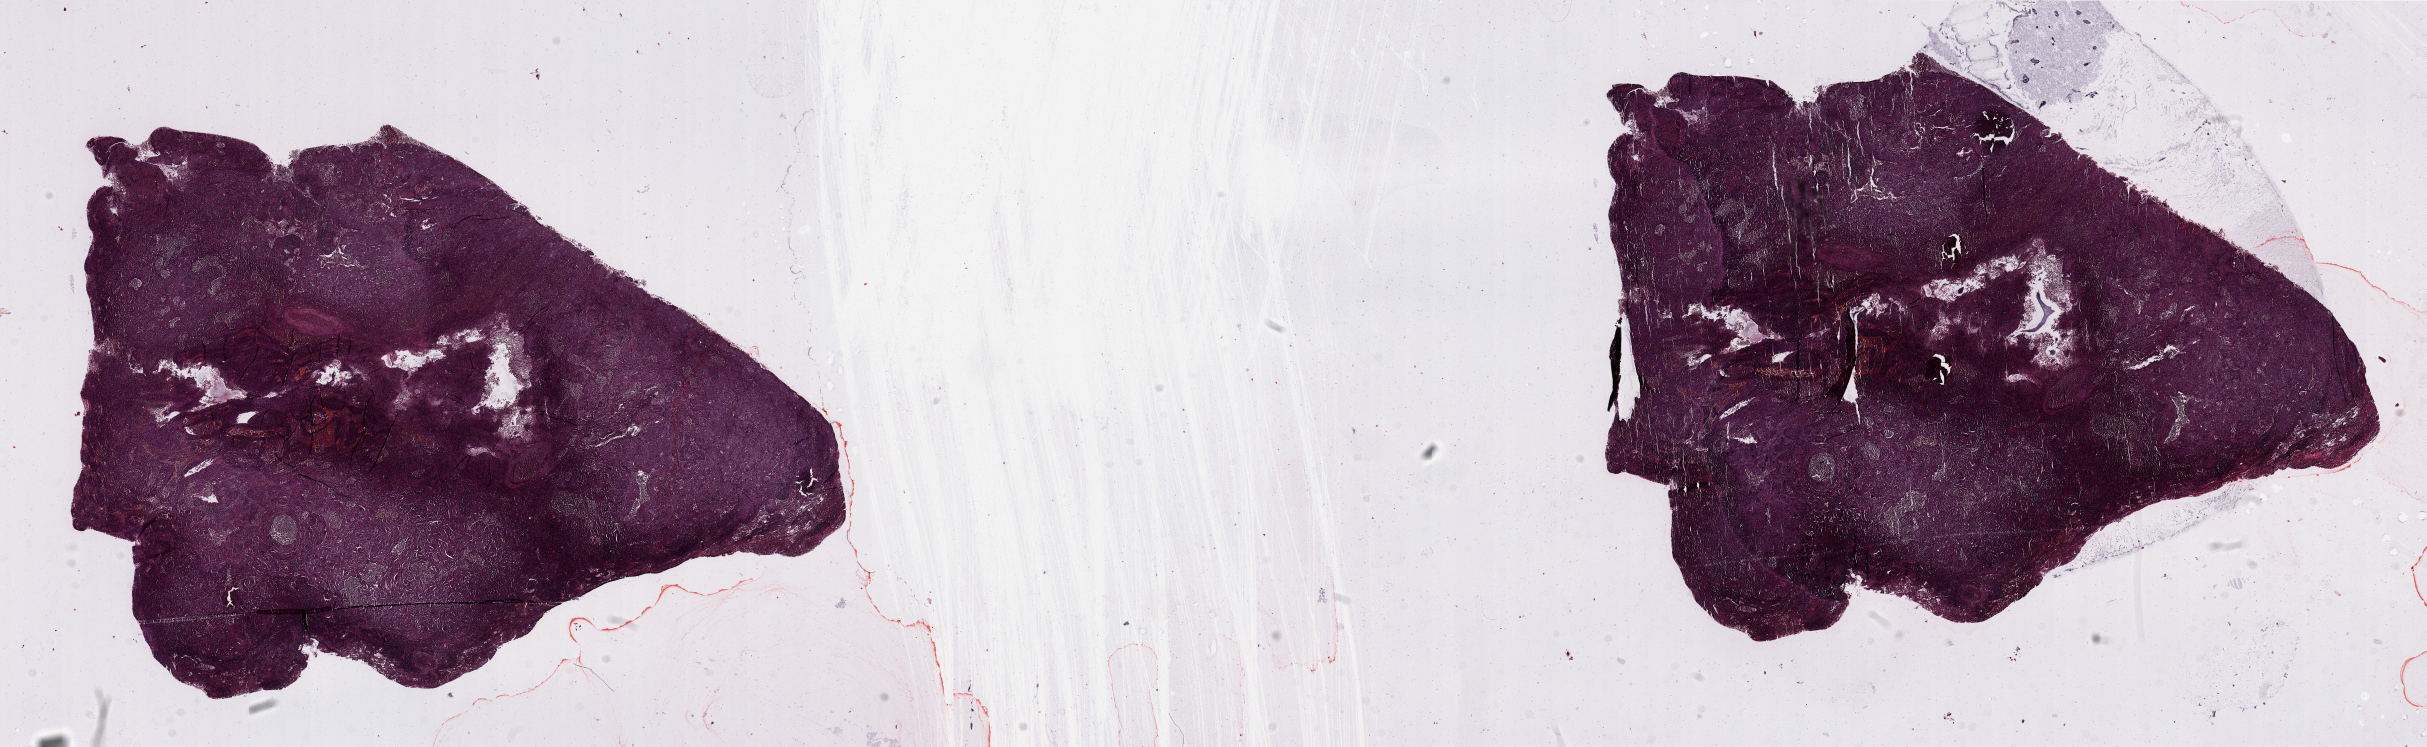
Digitized H&E-stained tissue section (whole slide) — low-resolution overview of the scanned area, about 38.4 x 11.8 mm; tumour tissue sample, lung. Male, 66 y/o. Histologic grade: G1 (well differentiated).
- AJCC pathologic stage: II
- histologic diagnosis: Squamous cell carcinoma, NOS